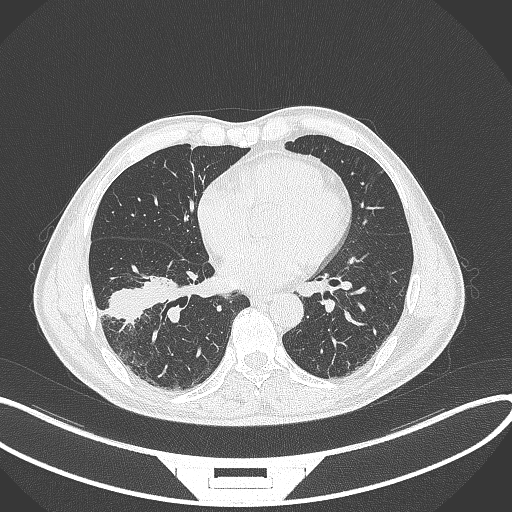
Chest CT, one axial slice; position 149 of 364 along the scan axis; reconstruction kernel B70f; lung window (W 1500 / L -600 HU); 1 mm slice thickness; 512 × 512 image matrix, field of view 400 × 400 mm. Male patient, age 58 years. Case-level facts recorded for this patient, not image findings: clinical TNM (as recorded): T3 N0 M0.
Structures marked on this image (rectangle marked by the reading radiologist):
- lung tumour (recorded histology: squamous cell carcinoma): bounding box (x1, y1, x2, y2) in pixels: (107, 268, 190, 323)